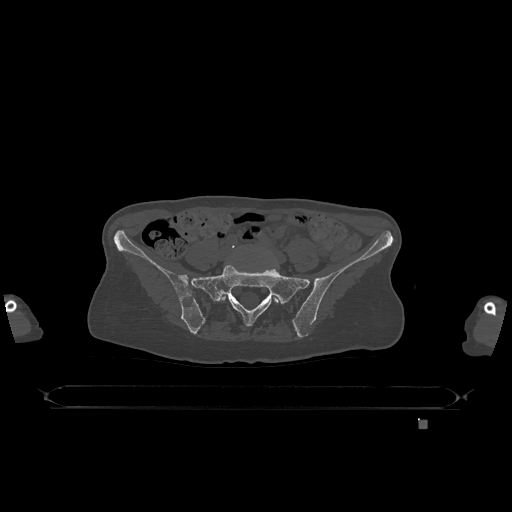
CT including the spine, one axial slice; position 200 of 1317 along the scan axis; bone window (W 1800 / L 400 HU); 0.5 mm slice thickness; 512 × 512 image matrix. Patient: female, 74 years. Case-level facts recorded for this patient, not image findings: primary cancer: lung.
Annotated regions visible in this slice (semi-automatically segmented with operator editing):
- L5 vertebra: bounding box (x1, y1, x2, y2) in pixels: (220, 294, 279, 303)